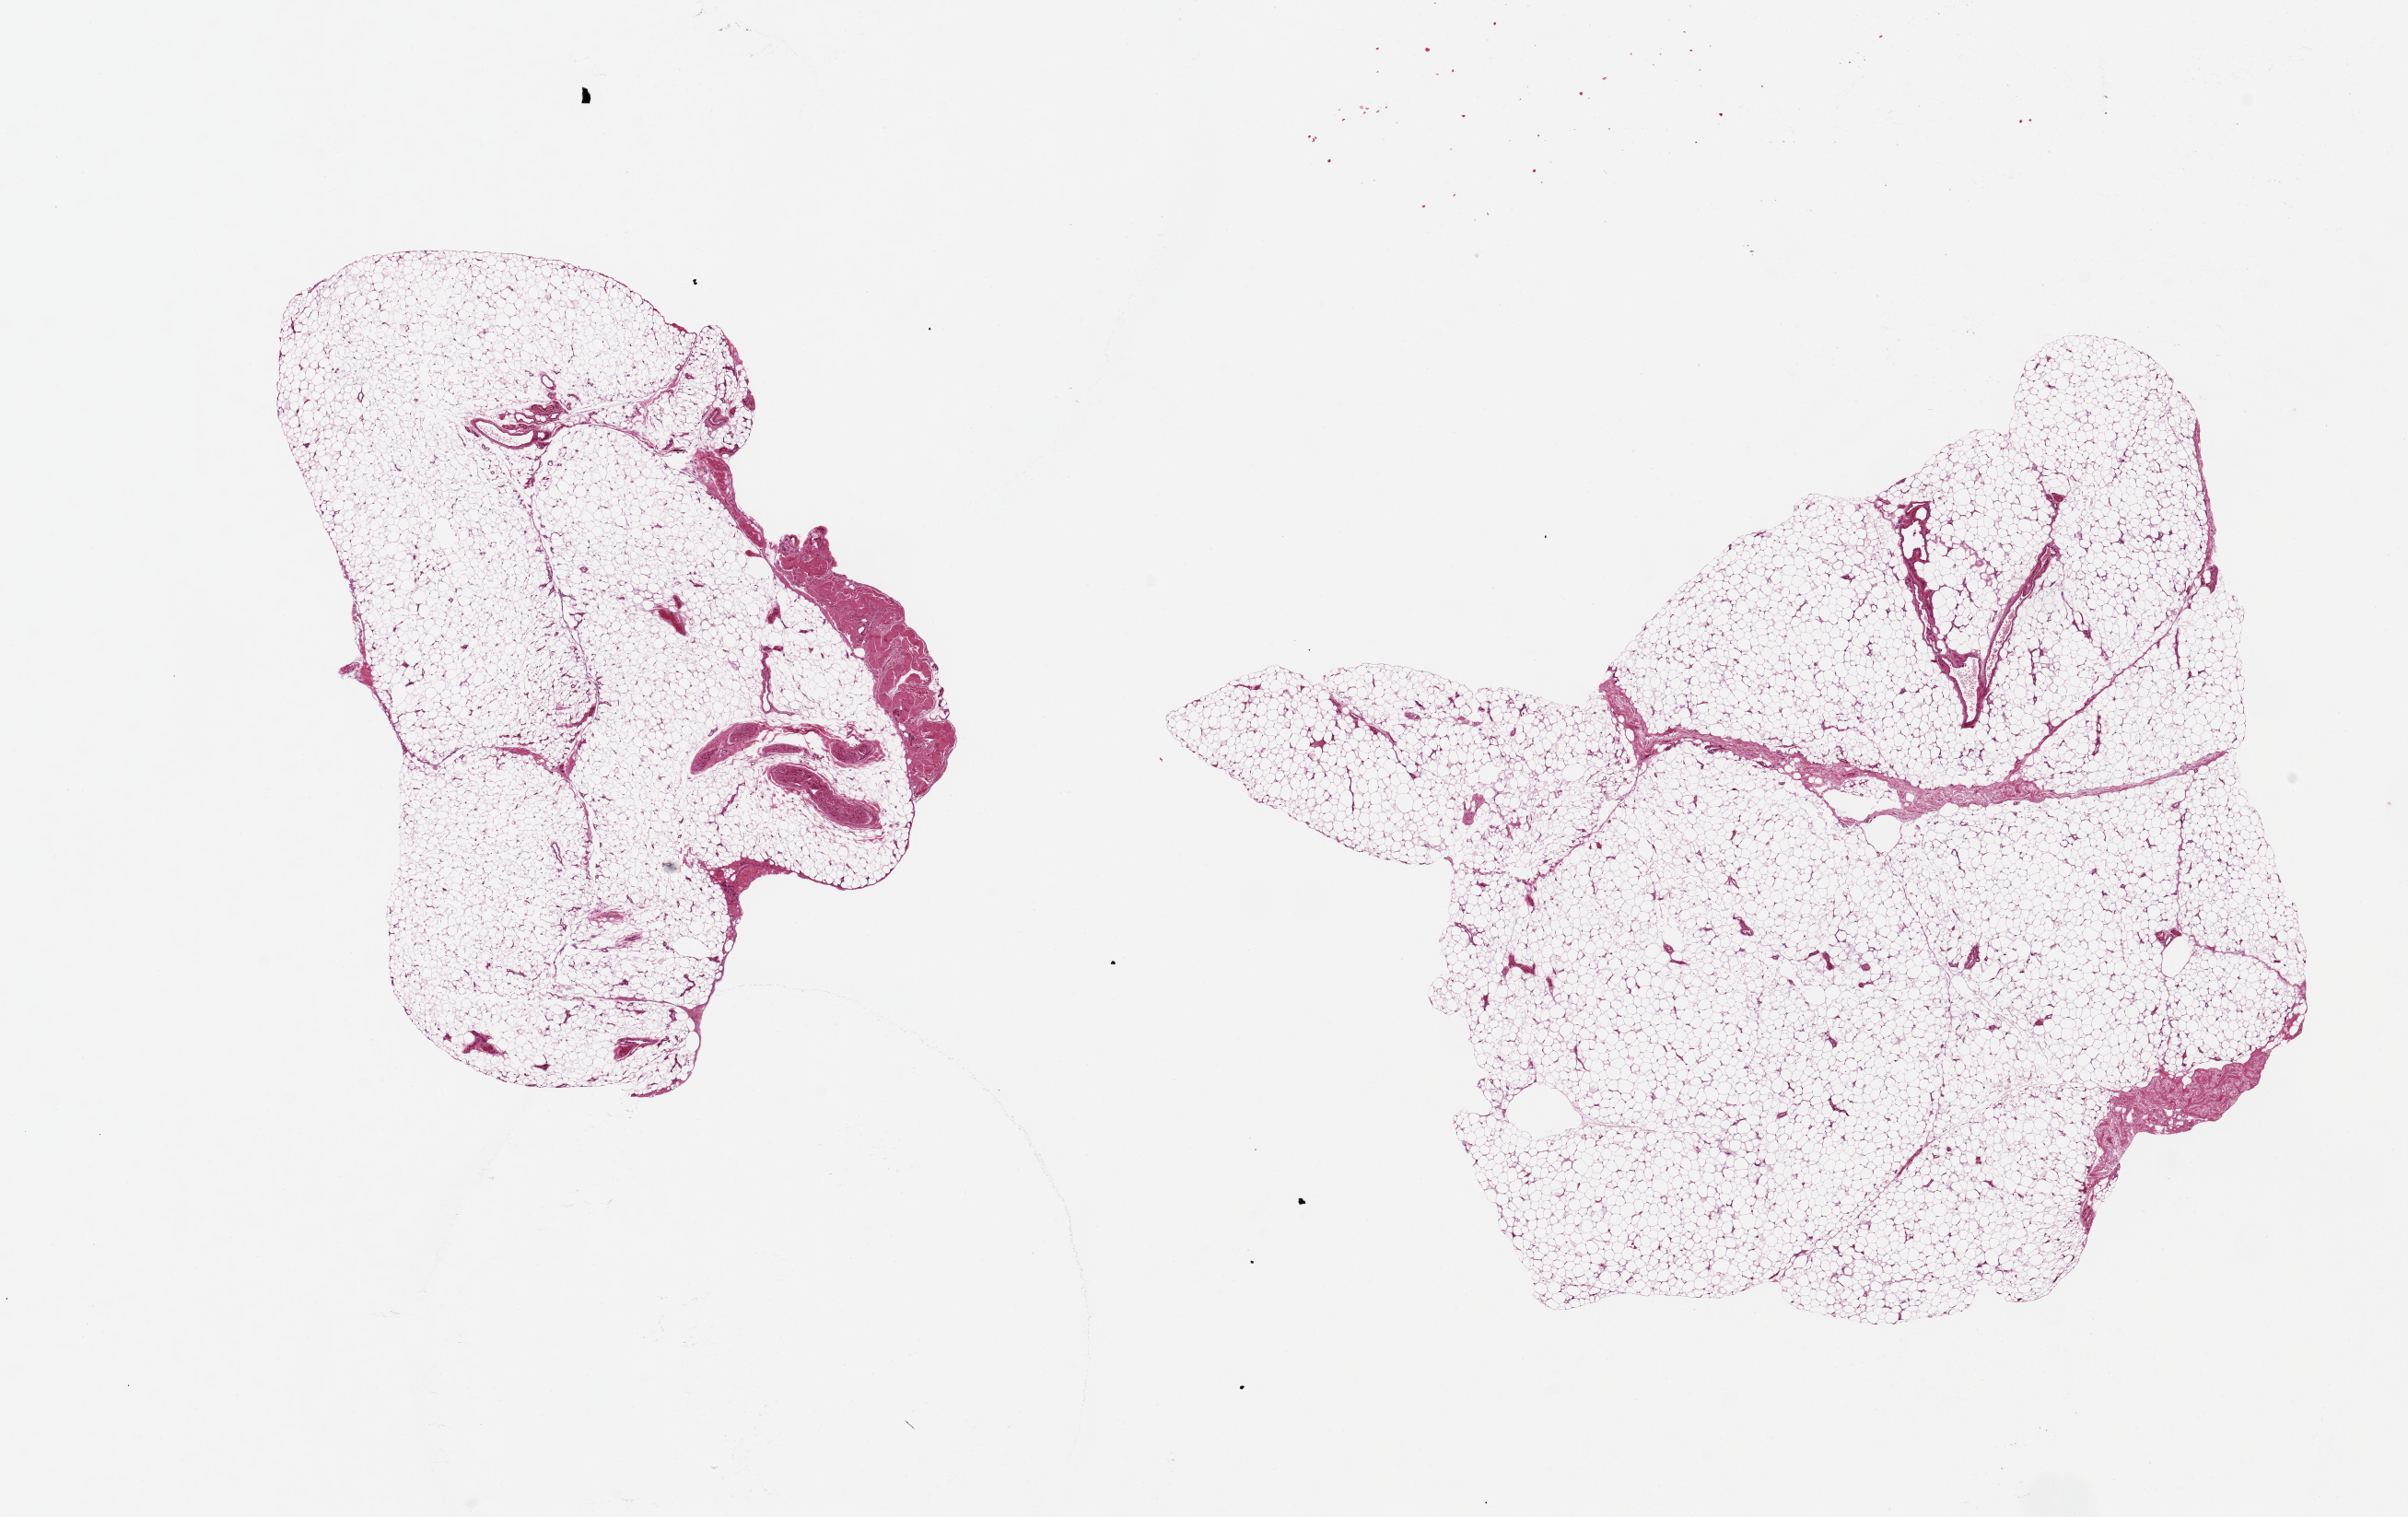
Whole-slide image, H&E stain, brightfield — a low-resolution overview of the entire scanned area, about 20.7 x 13.0 mm (slide scanned at 20x), PAXgene-fixed paraffin-embedded (PFPE) section, section of adipose tissue (target tissue), donor tissue sample. Donor sex: male.
Pathologist's review note for this sample: 2 pieces, 7.5x5 & 10x9.5mm.